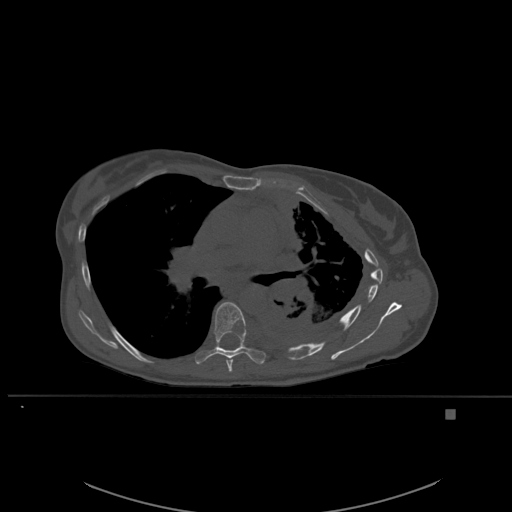
CT including the spine, one axial slice. Position 369 of 537 along the scan axis. Bone window (W 1800 / L 400 HU). 512 × 512 image matrix, field of view 440 × 440 mm. Patient: female, 45 years. Case-level facts recorded for this patient, not image findings: primary cancer: lung.
Annotated regions visible in this slice (semi-automatic segmentation, software-assisted and operator-edited):
- T6 vertebra: bounding box (x1, y1, x2, y2) in pixels: (226, 359, 233, 373)
- T7 vertebra: (196, 302, 266, 365)